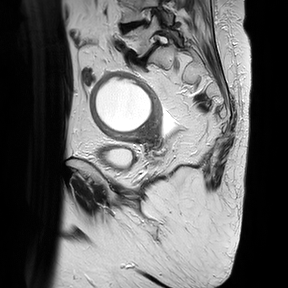
Pelvic MRI for cervical cancer, one sagittal slice; slice 11 of 30 in the series (ordered by position); T2-weighted; 1.5 T; TE 100 ms, TR 4816.3 ms; 4 mm slice thickness; 288 × 288 image matrix, field of view 300 × 300 mm. Patient: female, 74 years.
Annotated regions visible in this slice (outlined manually by an expert reader):
- uterus and cervix: box from (x=89, y=70) to (x=163, y=147) px